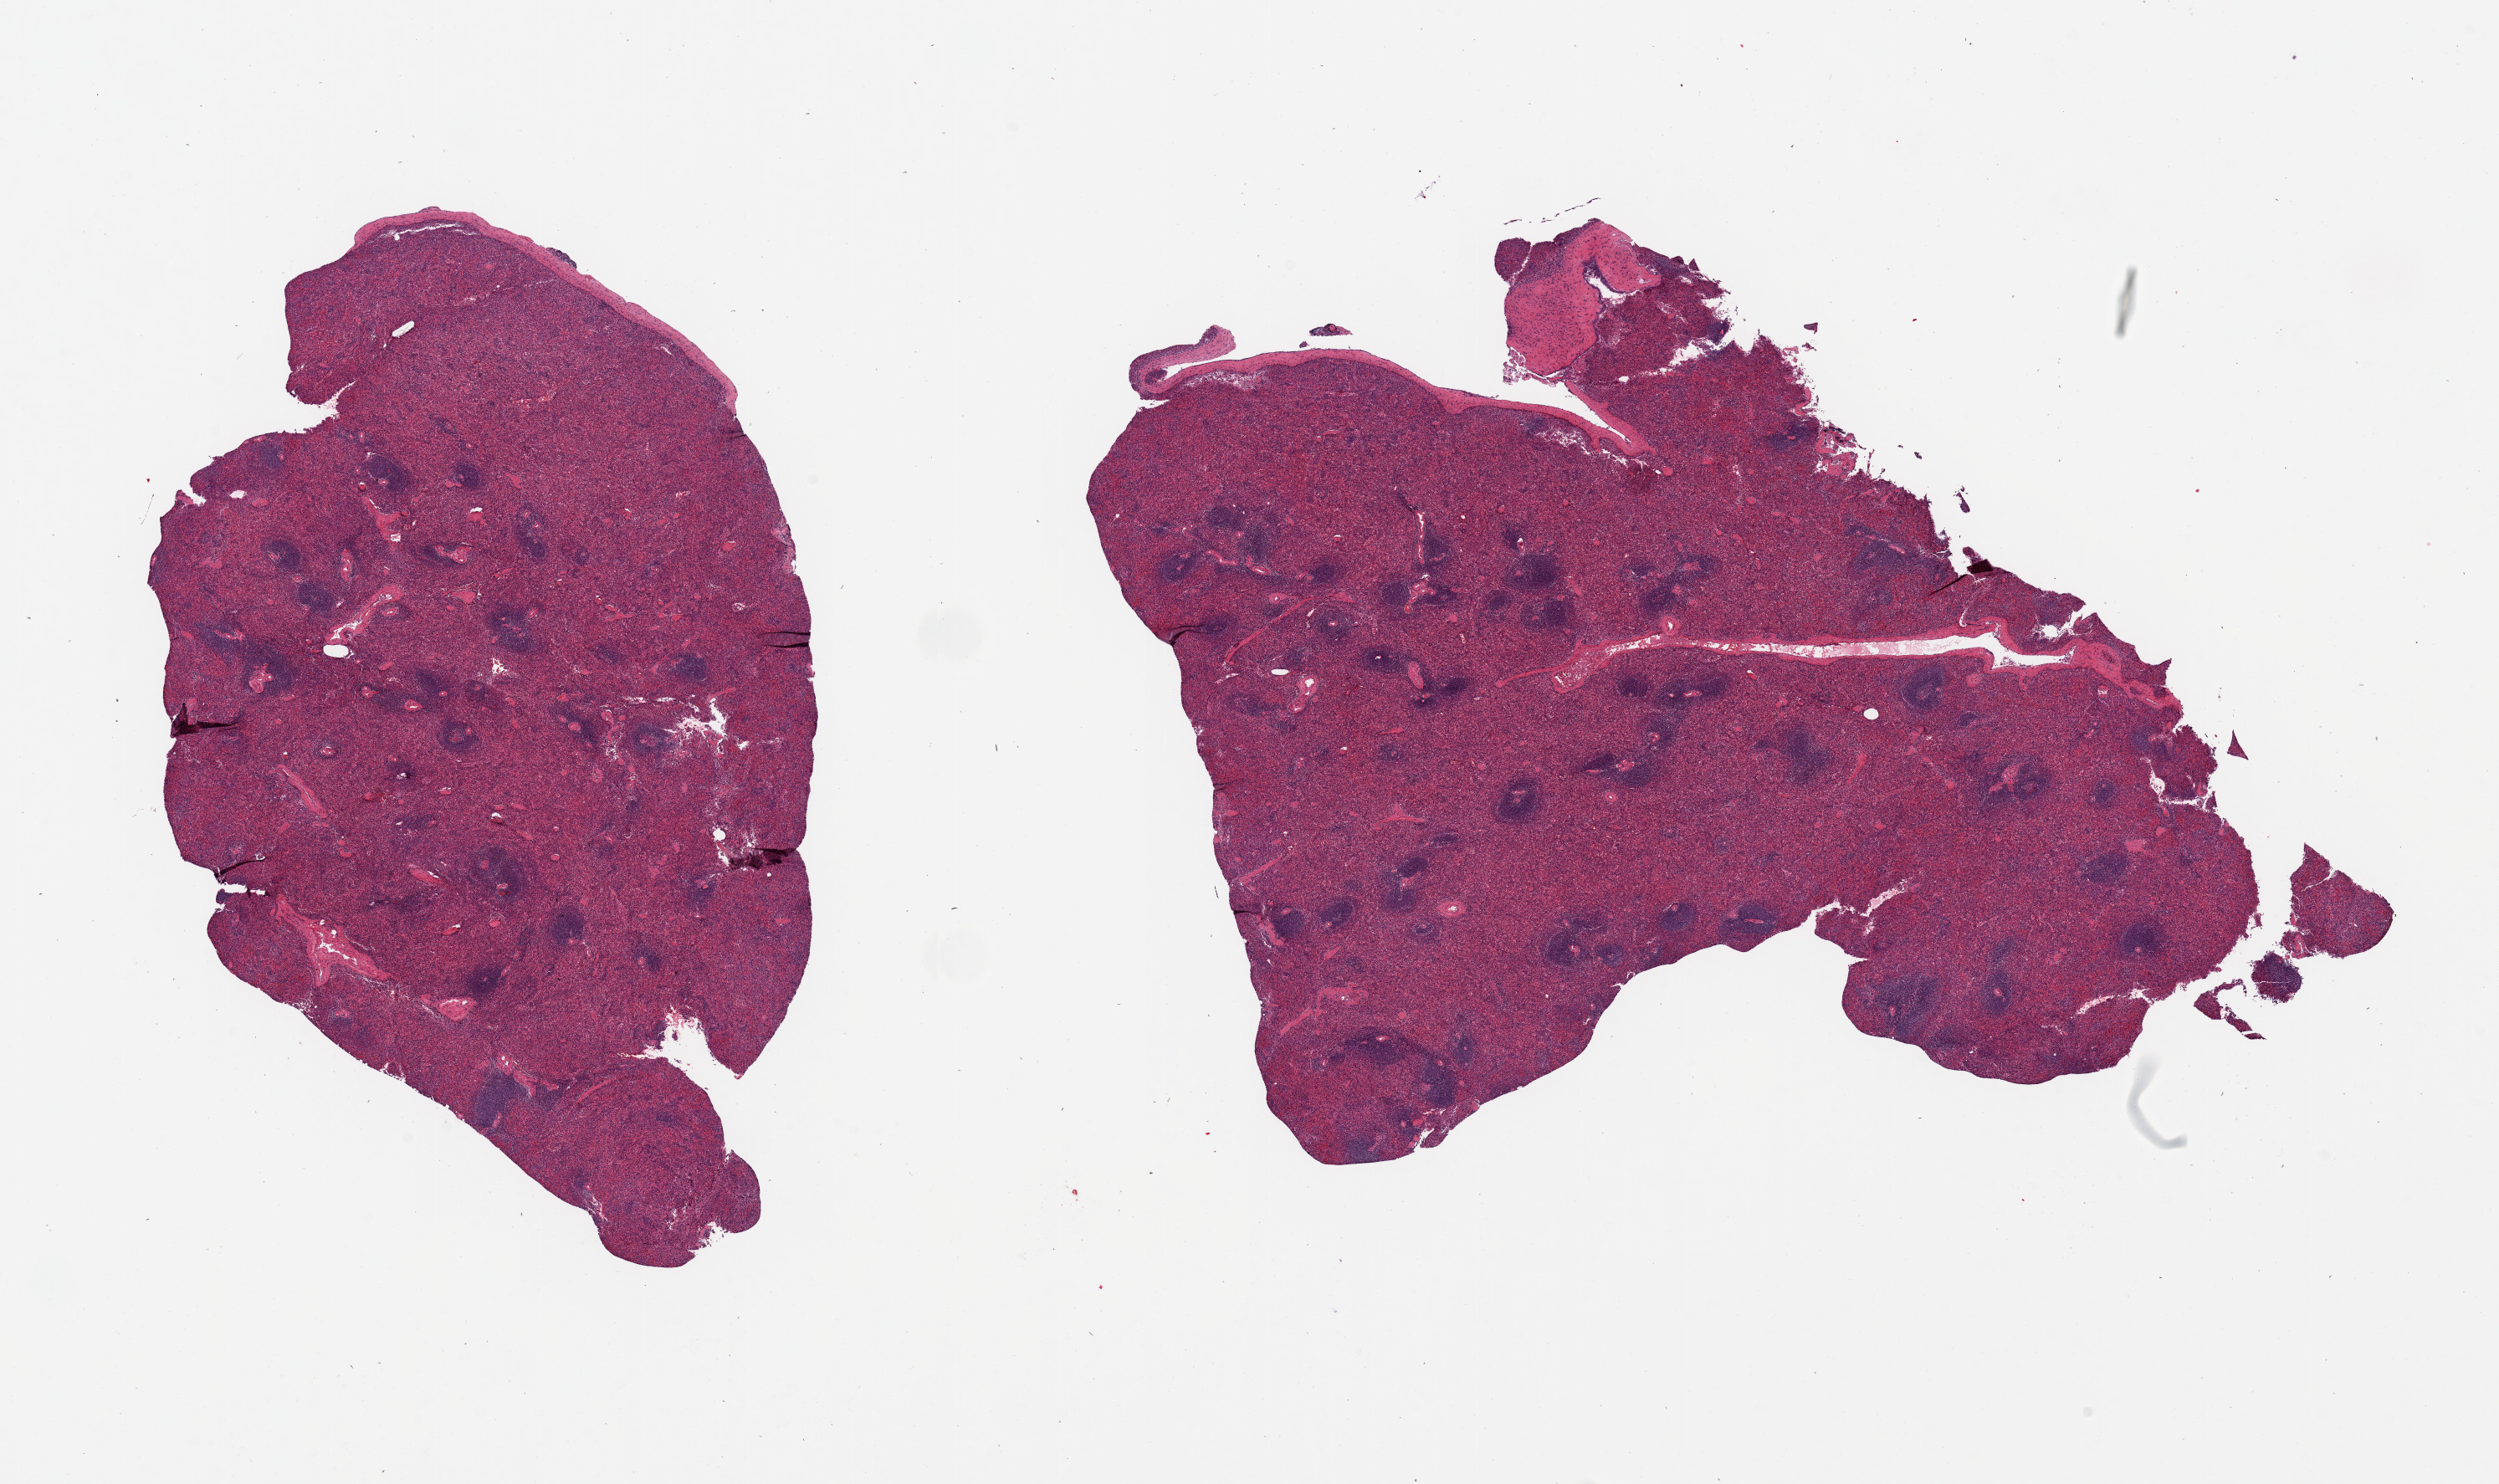
H&E whole-slide image — shown as a low-resolution overview of the whole scanned area (about 23.6 x 14.0 mm, from a 20x scan); PAXgene-fixed, paraffin-embedded tissue; sampled site (target tissue): spleen; tissue donor sample. Donor: female.
Review note (as recorded): 2 pieces, 7x7 & 9x8mm.